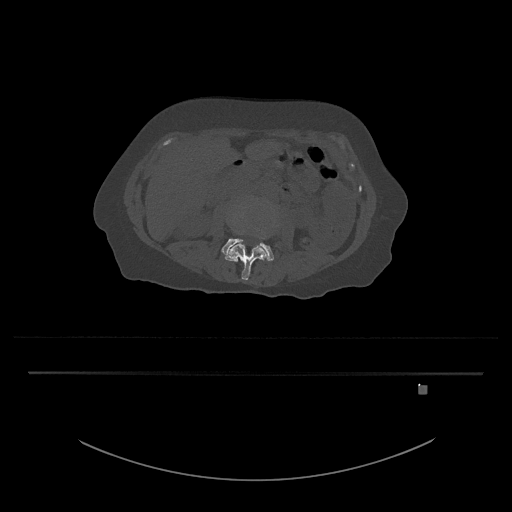
CT including the spine, one axial slice. Position 400 of 797 along the scan axis. Reconstruction kernel Br40s/3. Bone window (W 1800 / L 400 HU). 512 × 512 image matrix, field of view 500 × 500 mm. Patient: female, 57 years. Case-level facts recorded for this patient, not image findings: primary cancer: cervical.
Outlined on this slice (semi-automatically segmented with operator editing):
- L3 vertebra: bounding box [x1, y1, x2, y2] px = [224, 226, 267, 280]
- L4 vertebra: [221, 238, 274, 261]